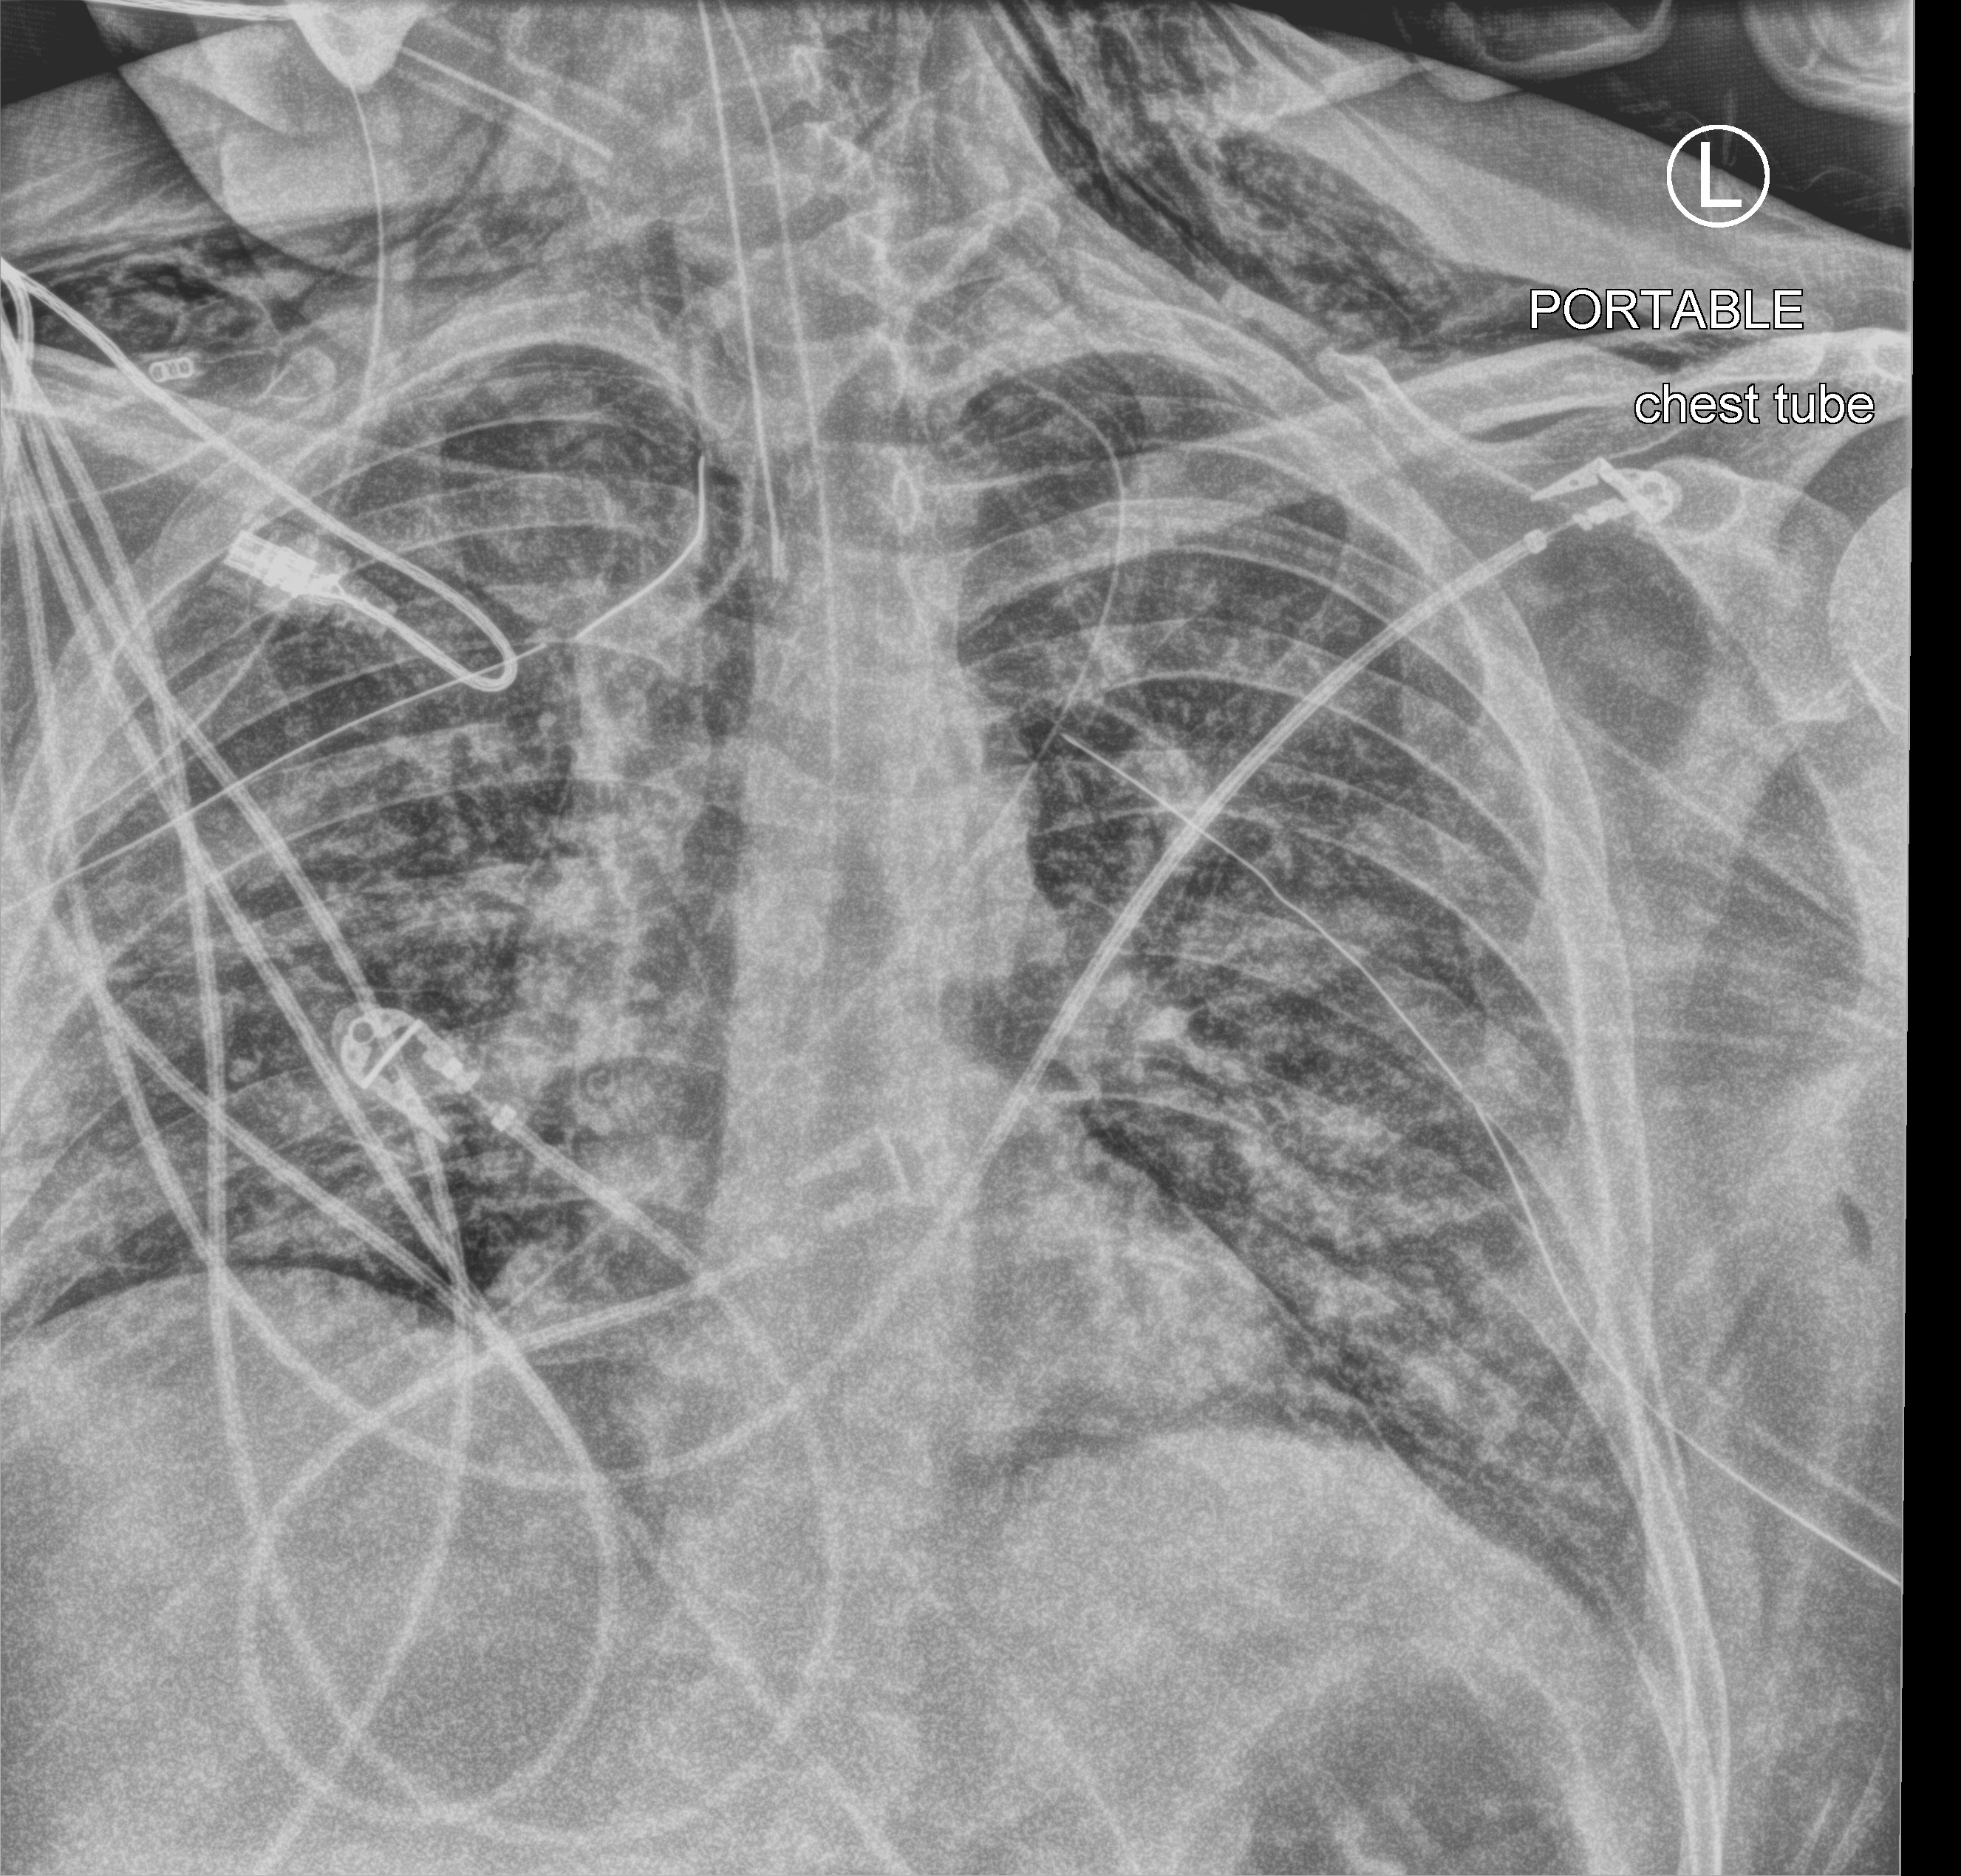
Chest X-ray (portable); anteroposterior (AP) projection. Patient hospitalised with COVID-19; male, aged 18–59 years.
Admission-level facts for this patient (not findings on this image; timing relative to this image not recorded): length of hospital stay: 63 days; chronic kidney disease (admission record): no; admitted to intensive care during this hospital stay: yes.